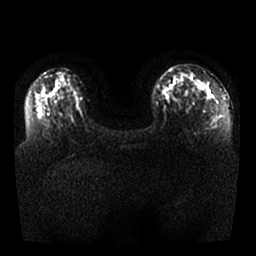
Breast MRI, one axial slice; slice 13 of 25 in the series (ordered by position); diffusion-weighted series; image 2 of 4 stored at this slice position (different b-values; order by instance number); 1.5 T; 4 mm slice thickness; 256 × 256 image matrix, field of view 340 × 340 mm. Female patient.
Structures marked on this image (manually delineated by an expert):
- tumour on diffusion-weighted imaging: box from (x=176, y=67) to (x=213, y=102) px